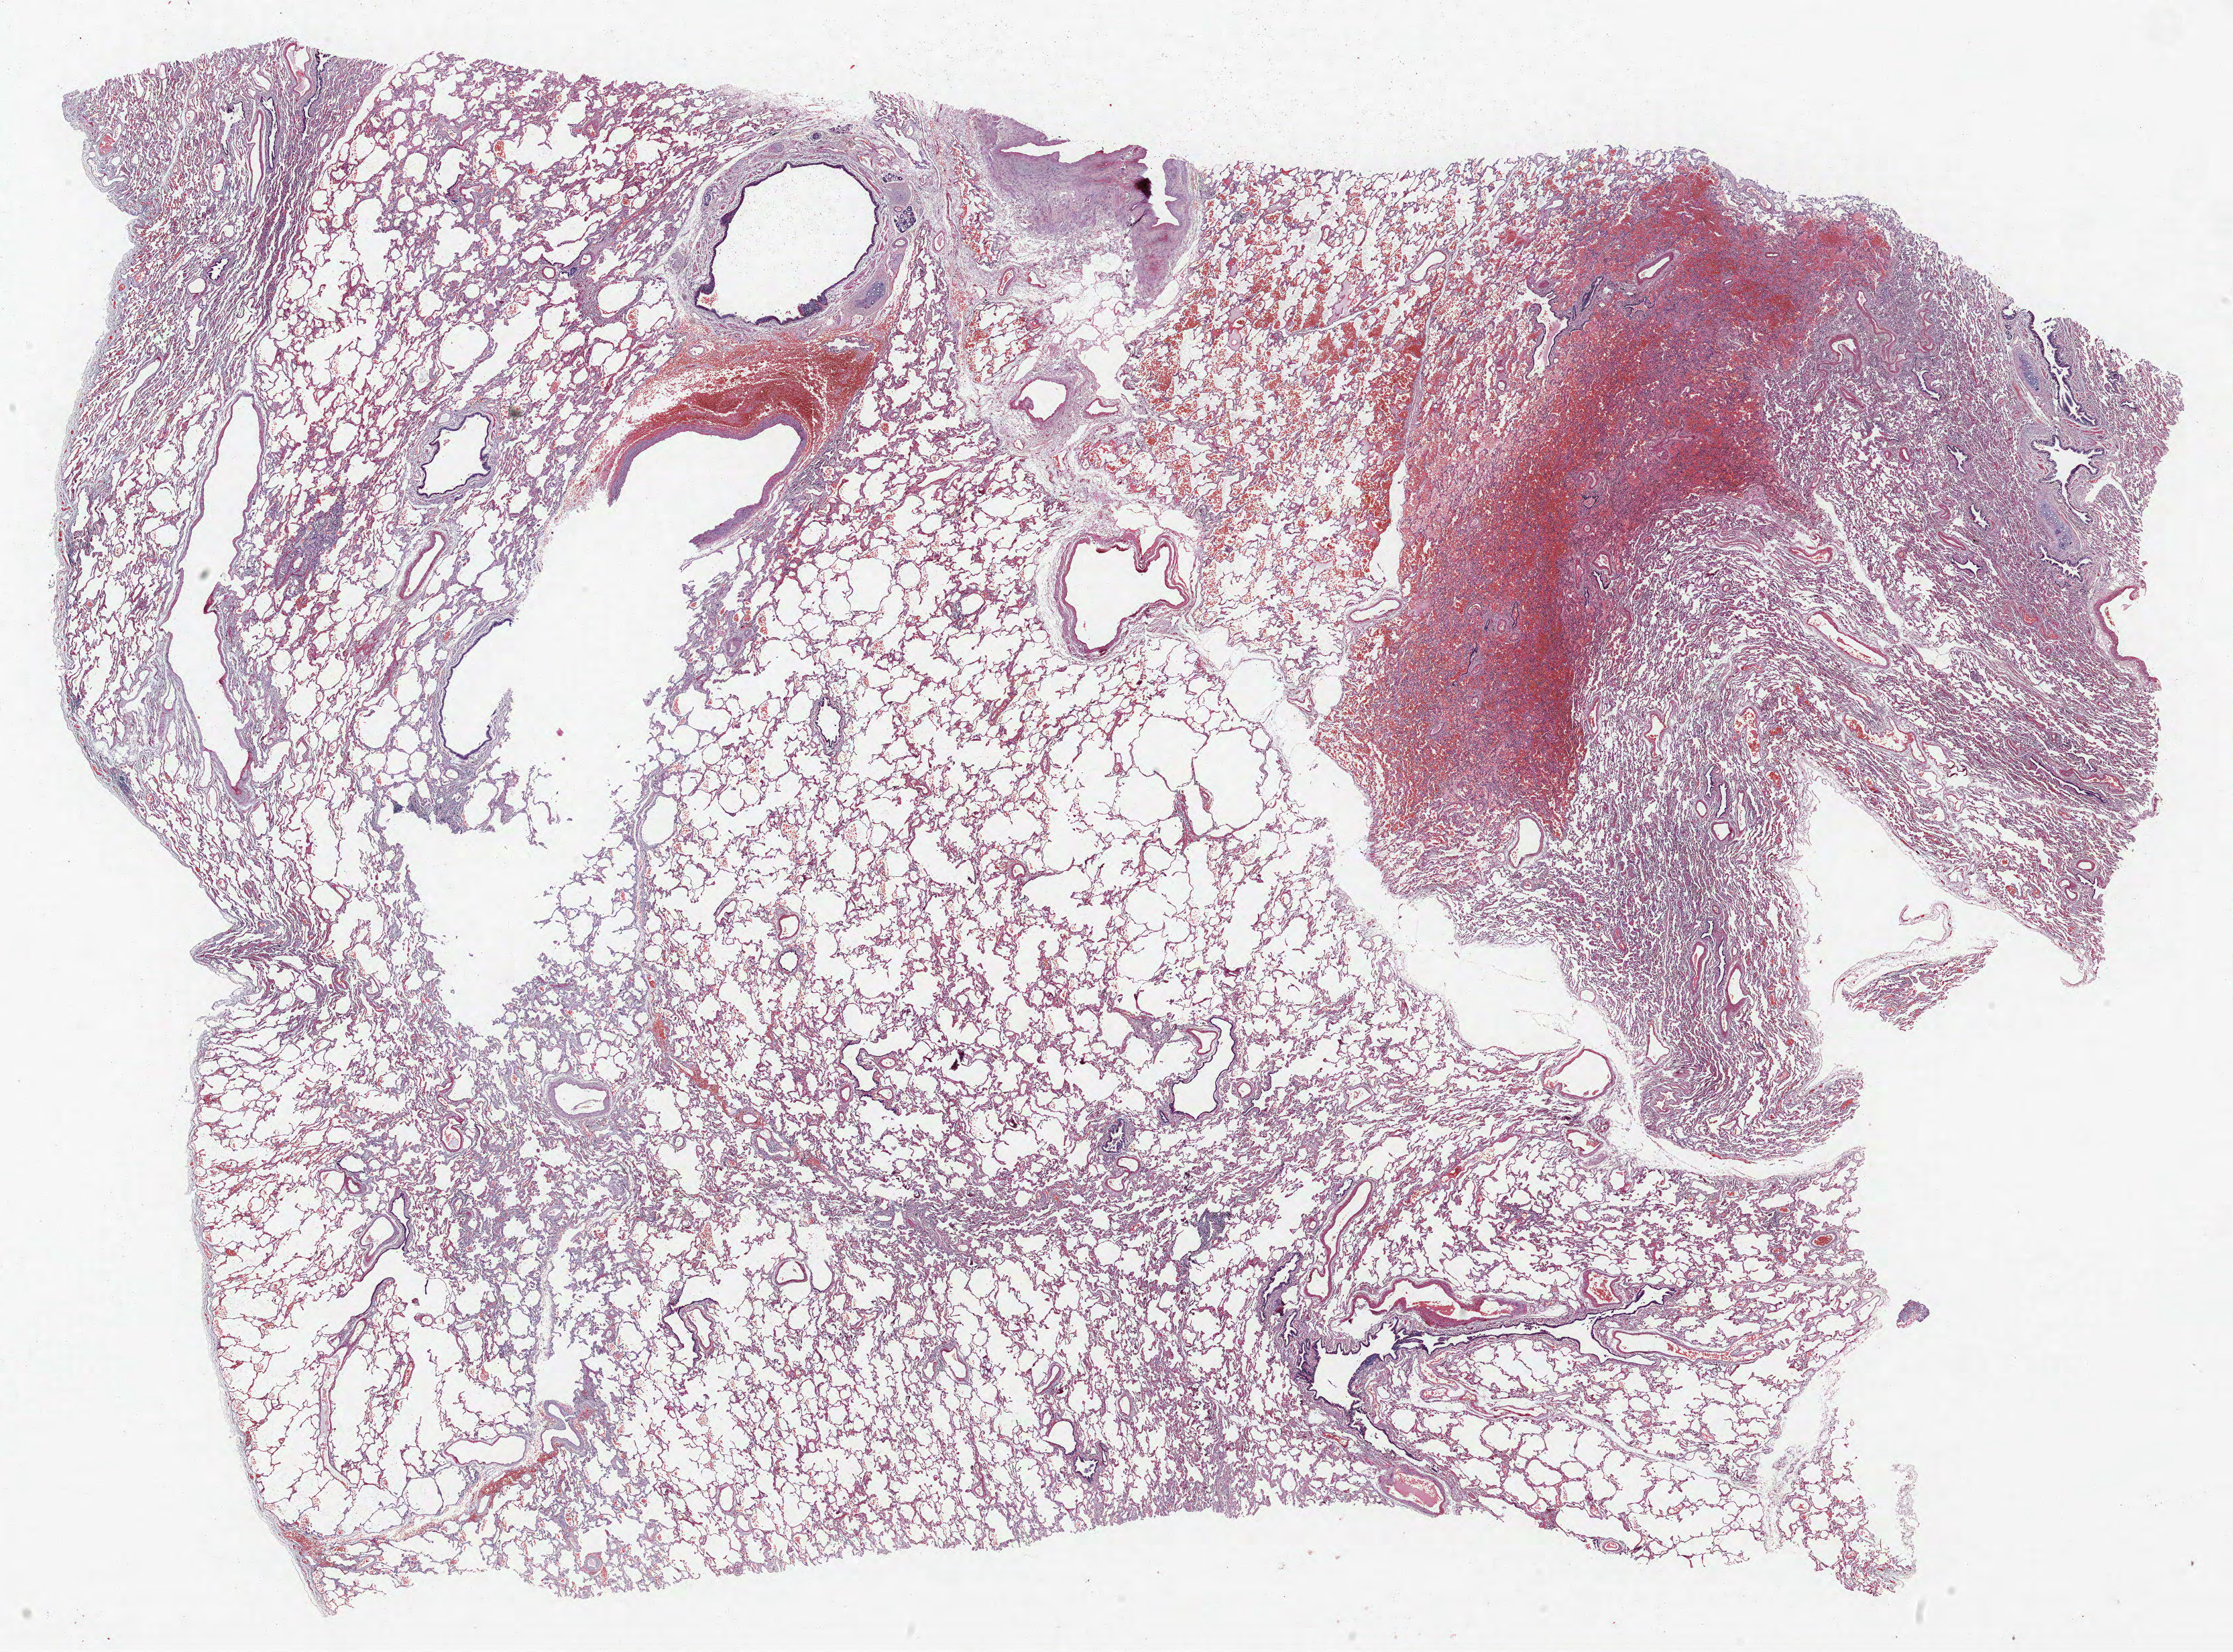
H&E whole-slide image, a low-resolution overview of the entire scanned area, about 26.6 x 19.7 mm (from a 40x scan), formalin-fixed paraffin-embedded (FFPE) section, lung. Female patient, aged 57 at enrolment. Former smoker at enrolment. Grade: well differentiated (G1).
* participant's lung-cancer diagnosis: Adenocarcinoma, NOS
* stage (AJCC 6th edition): IA
* primary tumour location (clinical record): right middle lobe
* tumour size (pathology): 21 mm